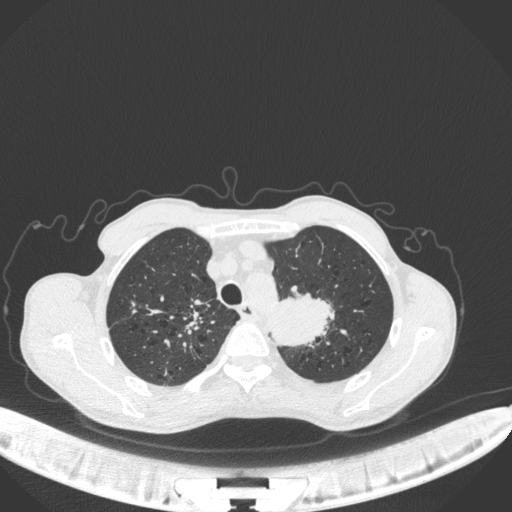
Chest CT, one axial slice; slice 342 of 394 in the series (ordered by position); reconstruction kernel B31f; 120 kVp; lung window (W 1500 / L -600 HU); 1 mm slice thickness; 512 × 512 image matrix, field of view 400 × 400 mm. Patient: male, 65 years. Case-level facts recorded for this patient, not image findings: clinical TNM (as recorded): T2b N0 M0.
Outlined on this slice (bounding box drawn by a radiologist):
- lung tumour (recorded histology: adenocarcinoma): bounding box [x1, y1, x2, y2] px = [267, 289, 333, 349]